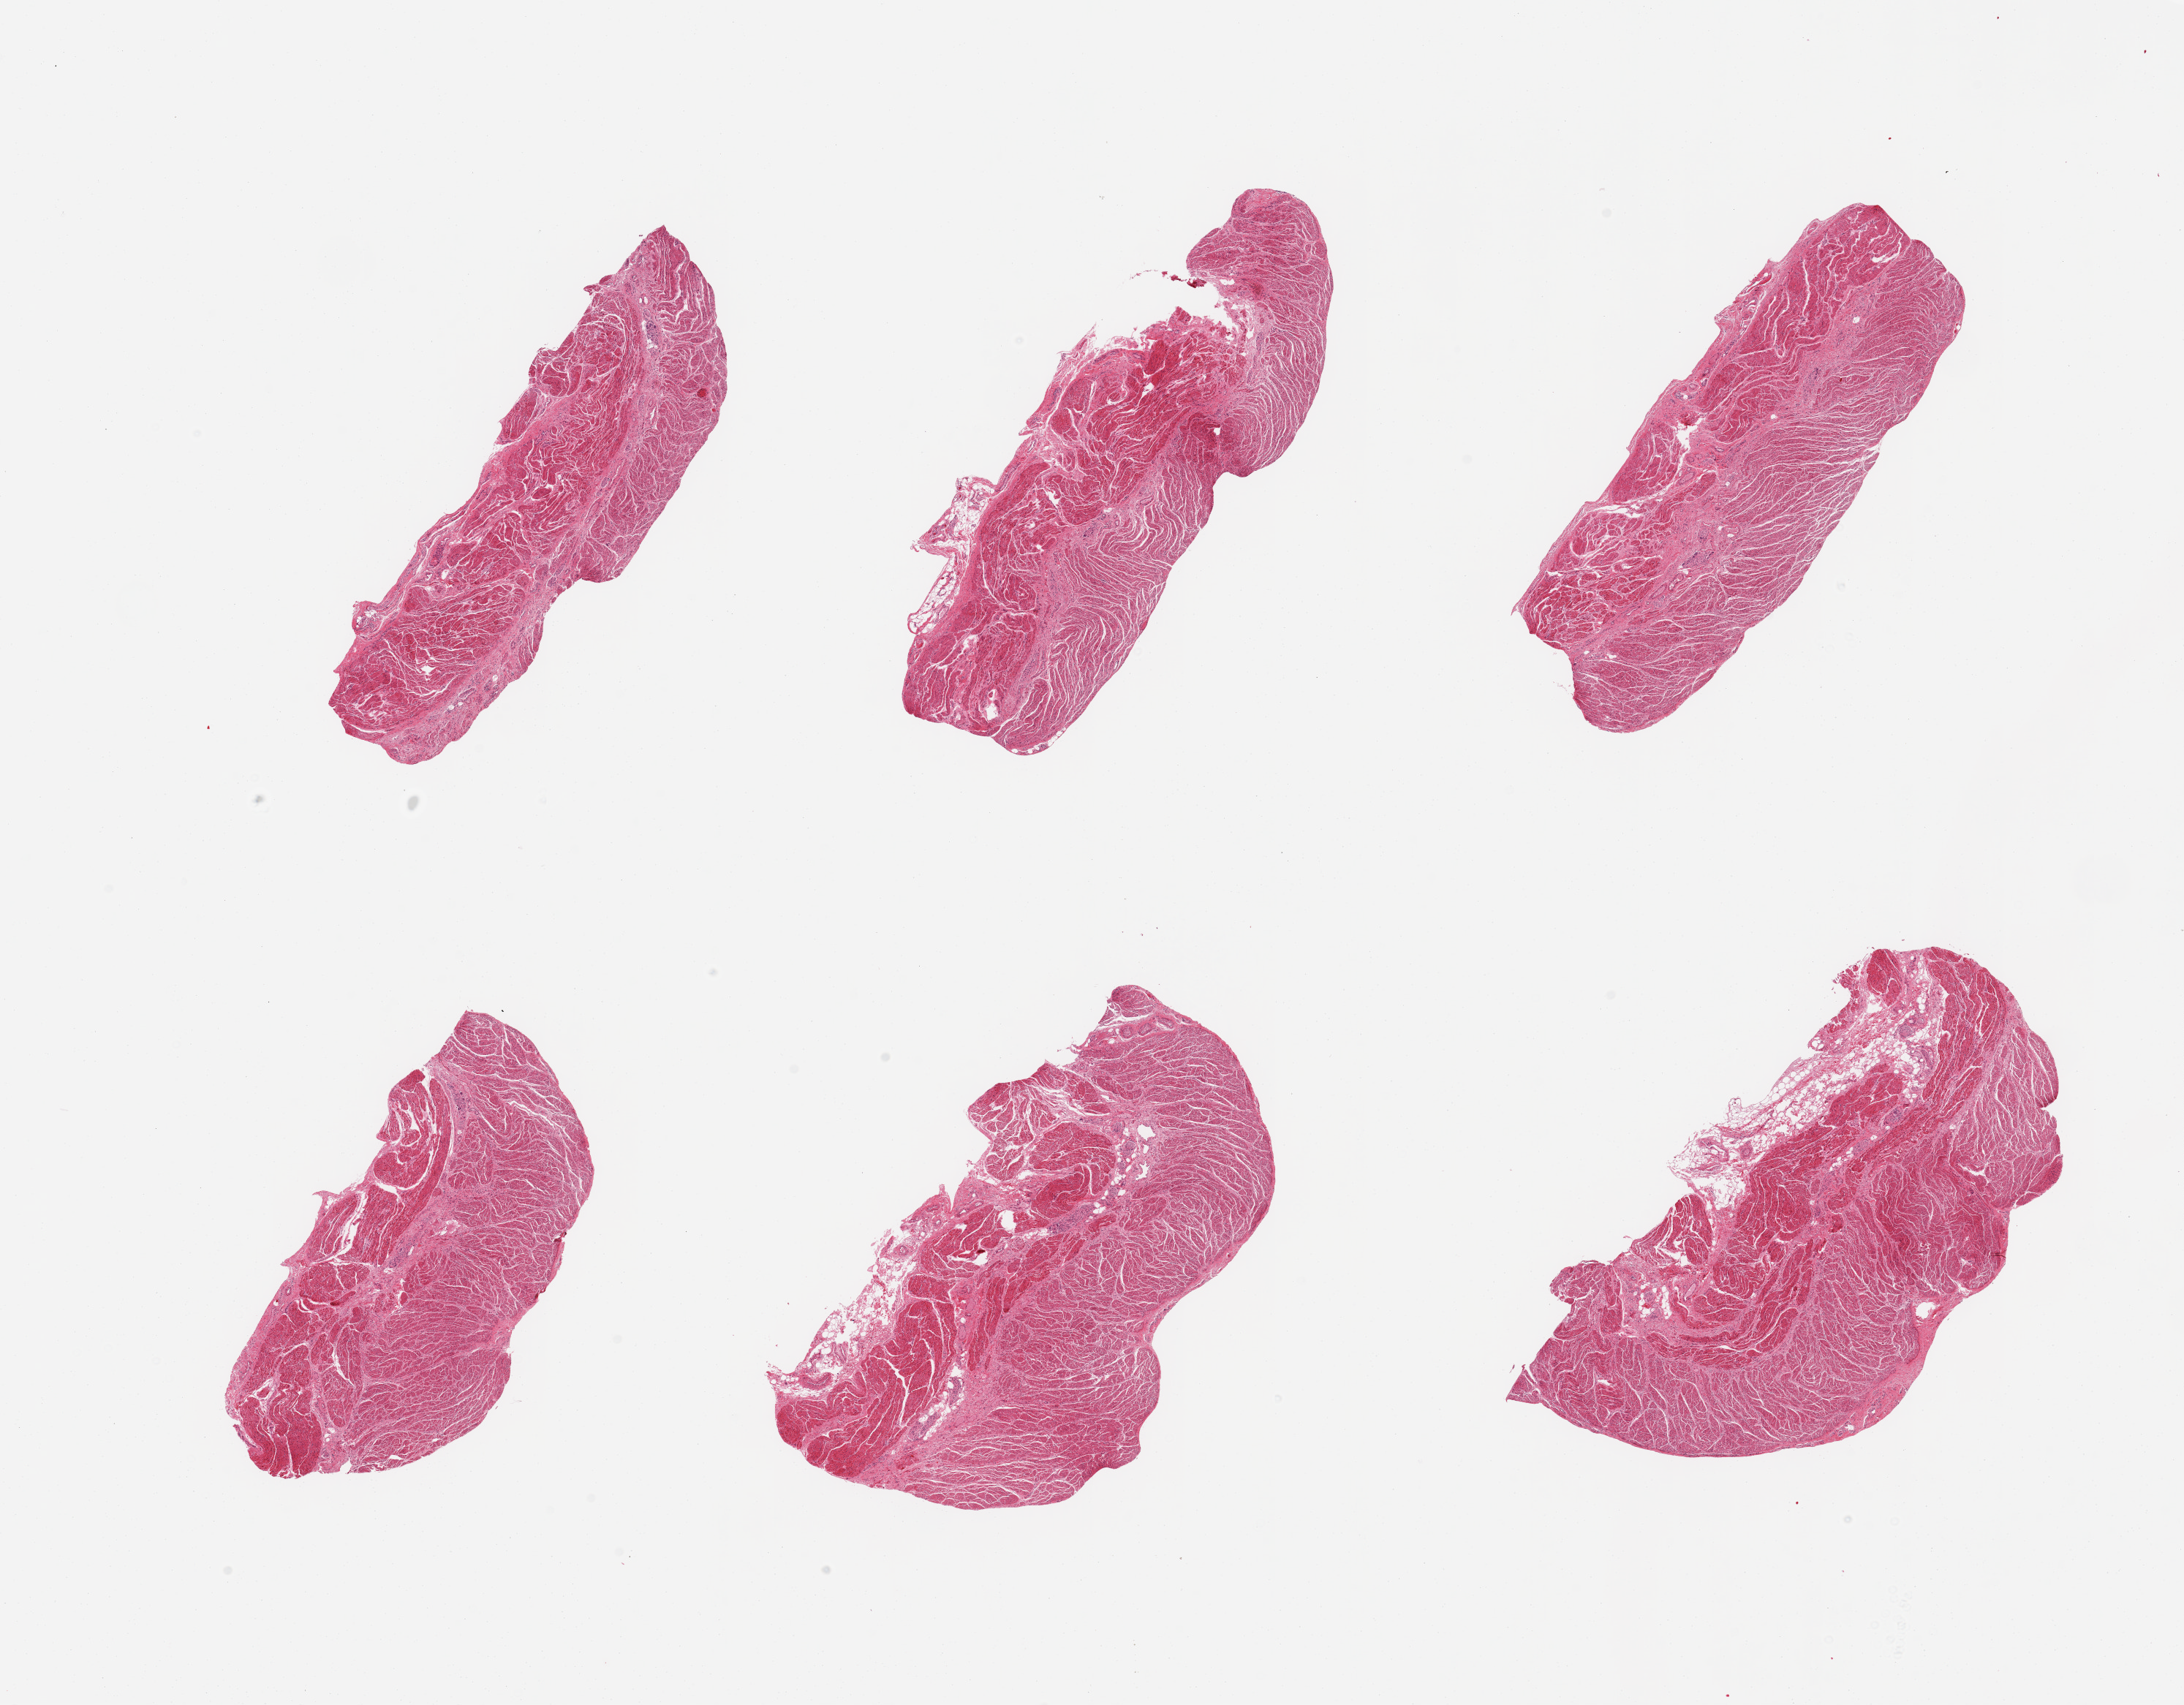
Digitized H&E-stained section, shown as a low-resolution overview of the whole scanned area (about 23.6 x 18.4 mm, from a 20x scan). PAXgene-fixed paraffin-embedded (PFPE) section. Target tissue: gastroesophageal junction. Tissue donor sample.
Review note (as recorded): 6 pieces; well dissected.